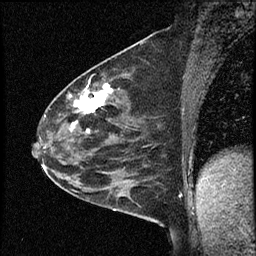
Breast MRI (dynamic contrast-enhanced), one sagittal slice. Slice 36 of 60 in the series (ordered by position). Dynamic contrast-enhanced study with each time point stored as its own series, time point 2 of 4 at this slice position (early post-contrast, ordered by acquisition time). 1.5 T. TE 4.2 ms, TR 17.6 ms. 2 mm slice thickness. 256 × 256 image matrix, field of view 200 × 200 mm. Patient: female, 53 years. Case-level facts recorded for this patient, not image findings: setting: breast cancer imaged before/during neoadjuvant chemotherapy; receptor status: HR-positive, HER2-negative.
Structures marked on this image (semi-automatic segmentation, software-assisted and operator-edited):
- analysis volume of interest (the breast-tissue region the enhancement analysis was run in; not a lesion): box from (x=42, y=69) to (x=156, y=199) px
- tumour enhancement mask (voxels above the 100 % enhancement threshold inside the analysis volume of interest): (x=70, y=84)–(x=113, y=133)